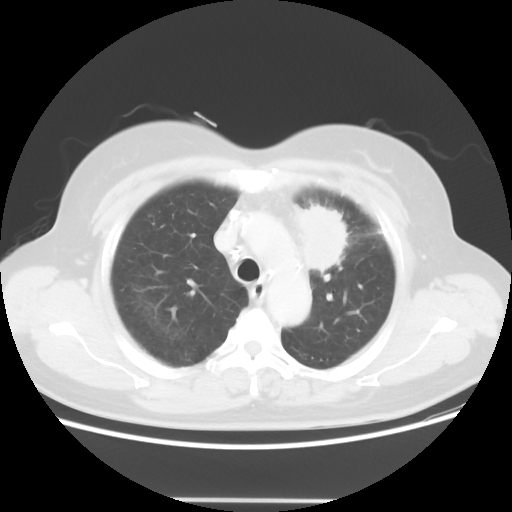
Chest CT, one axial slice; reconstruction kernel STANDARD; lung window (W 1500 / L -600 HU); 5 mm slice thickness; 512 × 512 image matrix, field of view 382 × 382 mm. Female patient, age 52 years. From the clinical record (not read from this slice): clinical TNM (as recorded): T2 N3 M0.
Structures marked on this image (rectangle marked by the reading radiologist):
- lung tumour (recorded histology: adenocarcinoma): bounding box (x1, y1, x2, y2) in pixels: (289, 197, 349, 271)